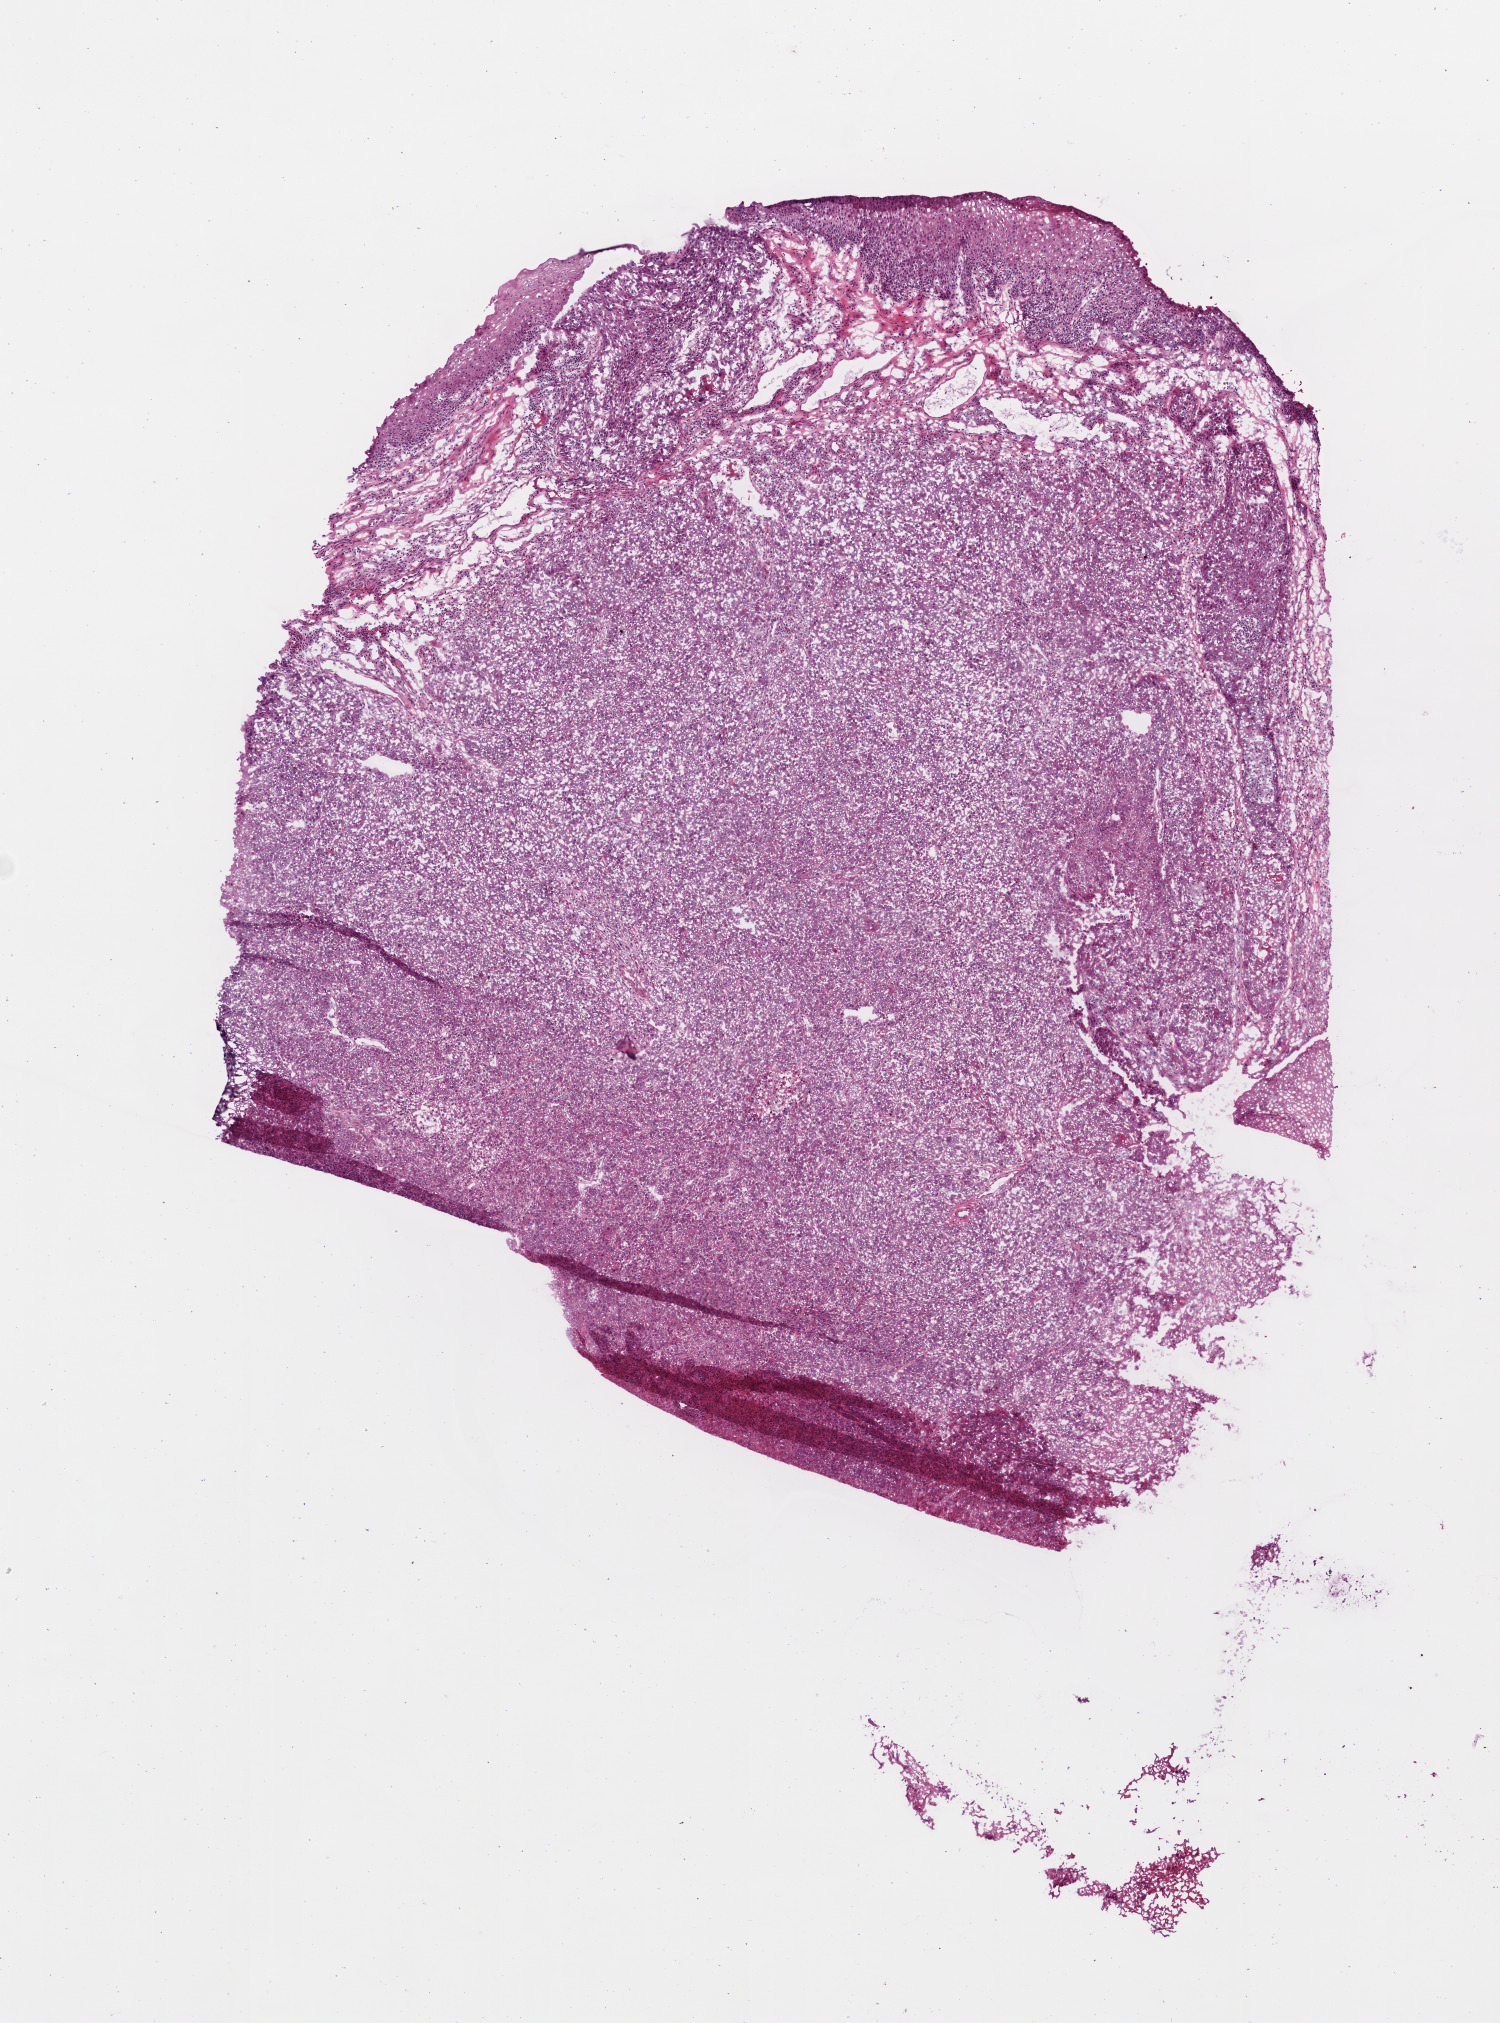
Whole-slide histology image, H&E, low-resolution overview of the scanned area, about 6.0 x 8.1 mm (slide scanned at 20x); frozen section from the bottom of the tissue portion; head and neck, primary tumour sample. Male patient; age at initial diagnosis 66 years. Histologic grade: G2 (moderately differentiated). Pathologist review of this section (percent, as recorded): tumour cells 90%, tumour nuclei 75%, normal cells 5%, stromal cells 5%, necrosis 0%. Inflammatory infiltration, as recorded: lymphocyte infiltration 1%, neutrophil infiltration 10%.
AJCC pathologic stage: IVA (7th edition). Histologic diagnosis: Squamous cell carcinoma, NOS (hypopharynx, NOS).